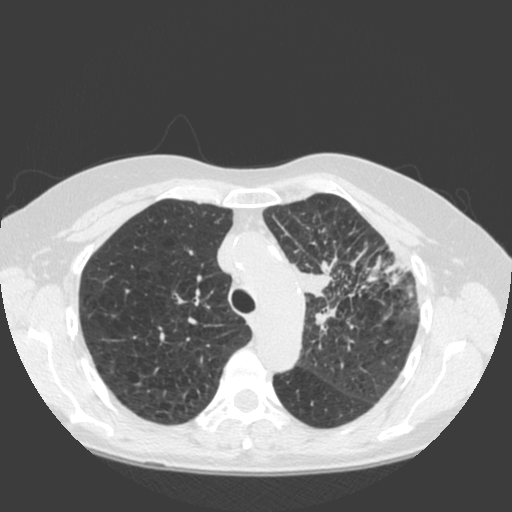
Low-dose screening chest CT, one axial slice. 120 kVp. Lung window (W 1500 / L -600 HU). 2 mm slice thickness. 512 × 512 image matrix, field of view 350 × 350 mm.
Annotated regions visible in this slice (expert manual segmentation):
- lesion 1 (tumor, hilum of left lung): bounding box [x1, y1, x2, y2] px = [295, 266, 332, 297]